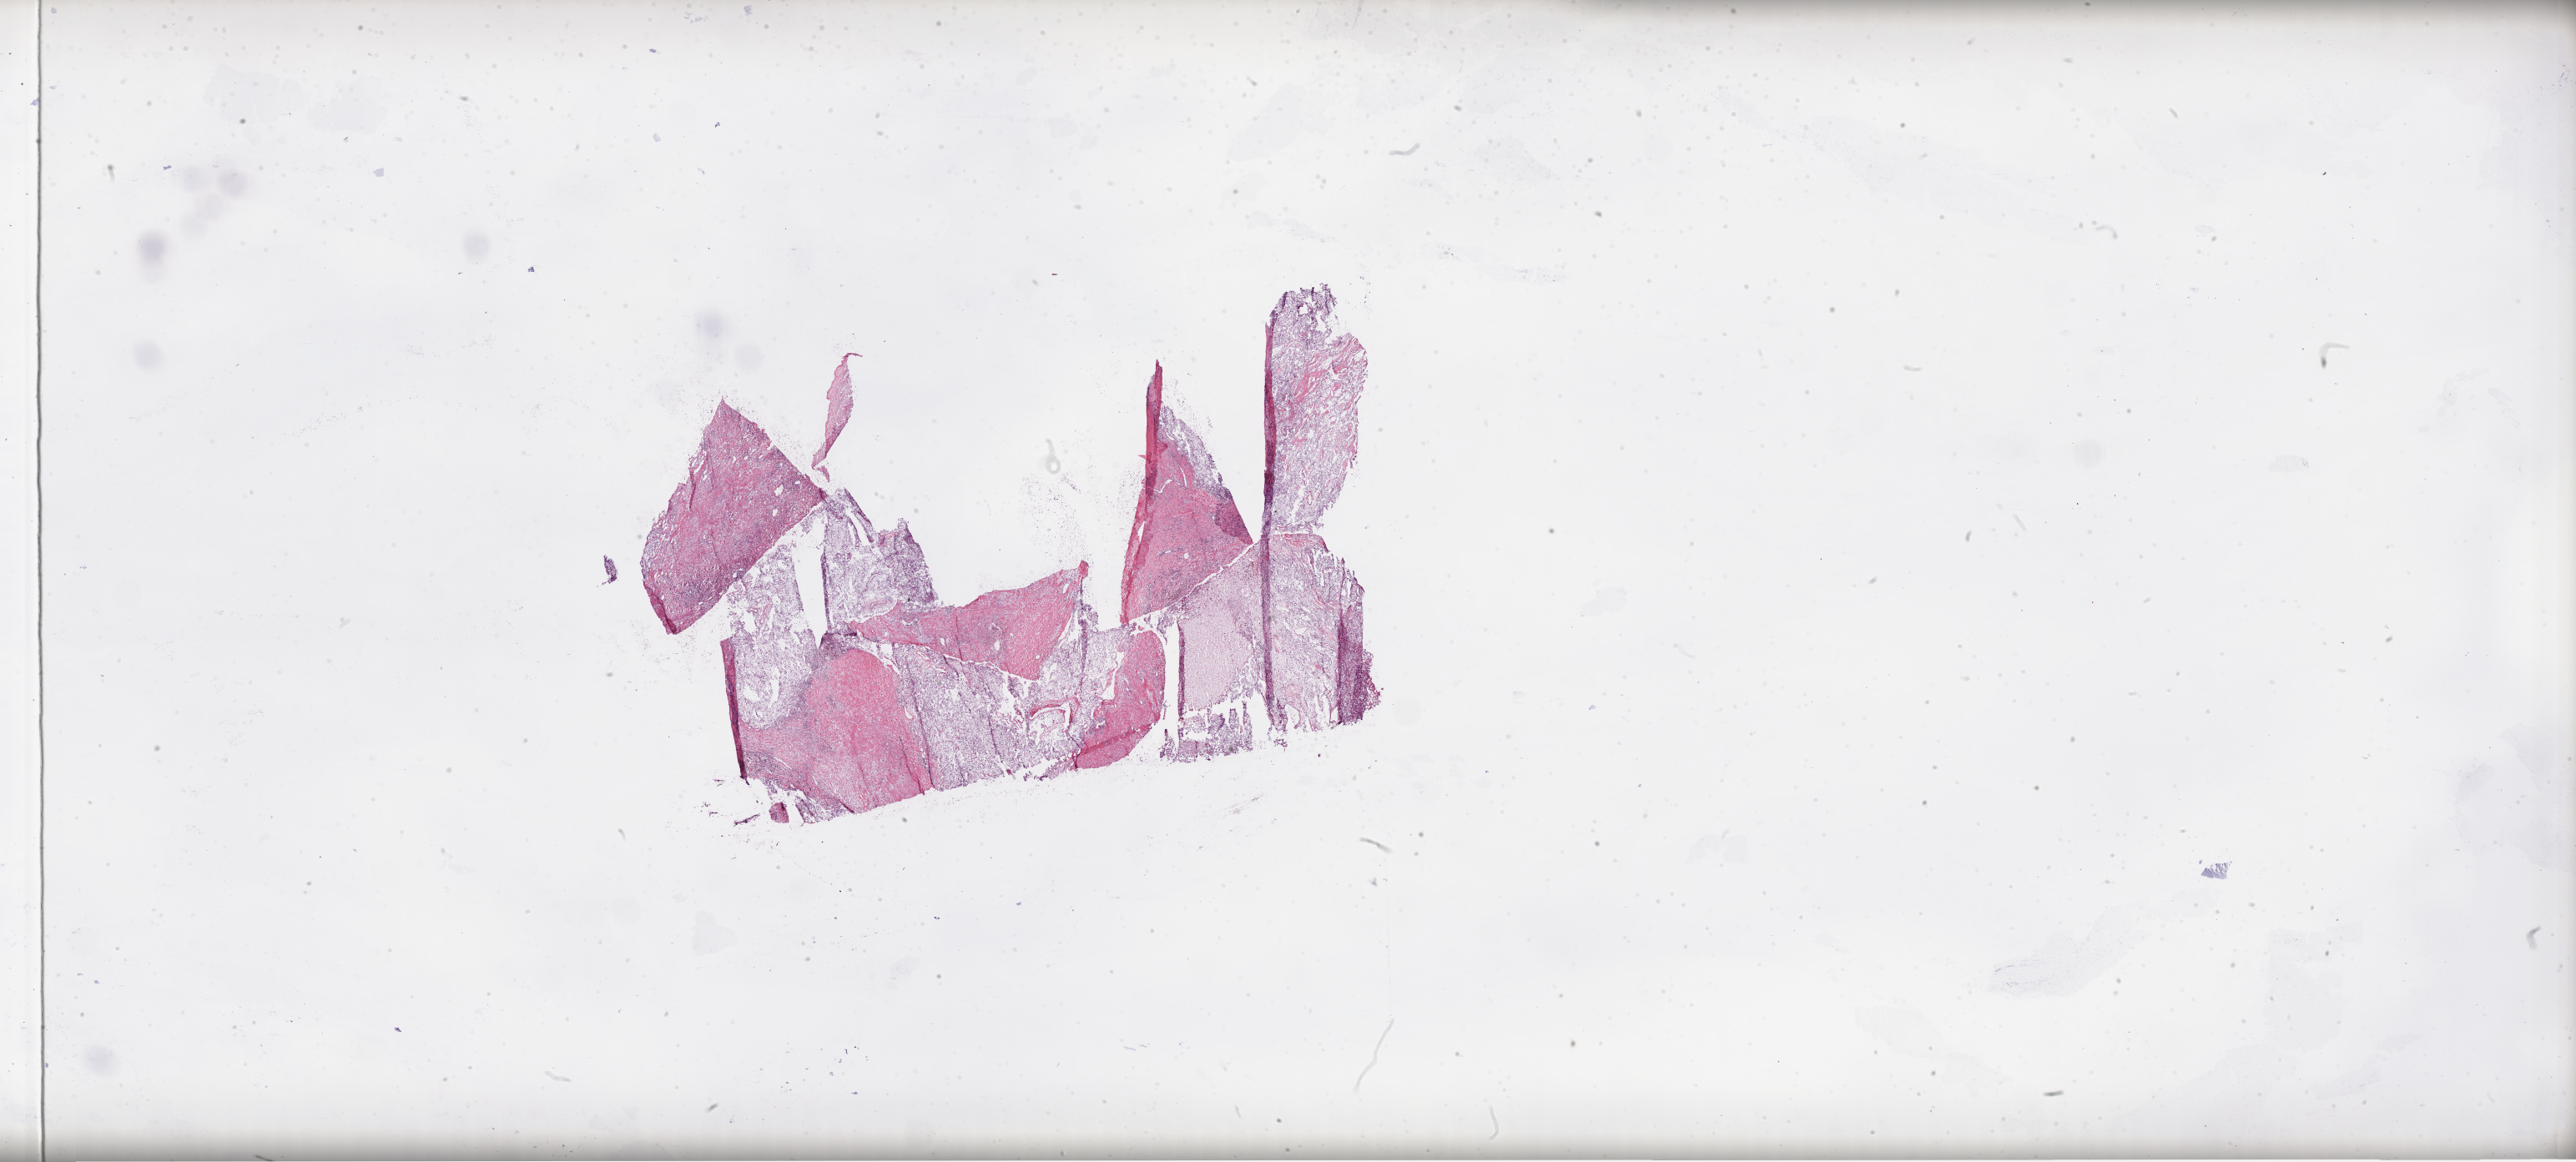
Hematoxylin and eosin (H&E) stained whole-slide image, shown as a low-resolution overview of the whole scanned area (about 49.8 x 22.5 mm), frozen section, primary tumour sample from the kidney. Patient: male, age at initial diagnosis 51 years. Histologic grade: G3 (poorly differentiated). Slide review estimates, as recorded: tumour cells 50%, tumour nuclei 75%, normal cells 0%, stromal cells 50%, necrosis 0%.
TNM: T1a NX M0. Pathologic diagnosis: Clear cell adenocarcinoma, NOS. AJCC pathologic stage: I (7th edition).